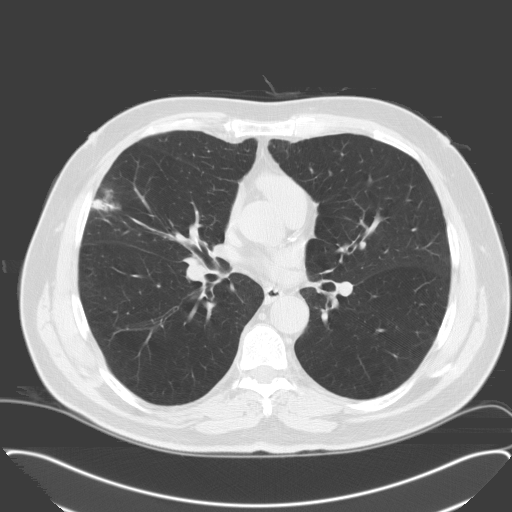
Low-dose screening chest CT, one axial slice; position 94 of 174 along the scan axis; lung window (W 1500 / L -600 HU); 3.2 mm slice thickness; 512 × 512 image matrix, field of view 400 × 400 mm.
Outlined on this slice (expert manual segmentation):
- lesion 1 (tumor, middle lobe of right lung): bounding box (x1, y1, x2, y2) in pixels: (92, 190, 118, 211)